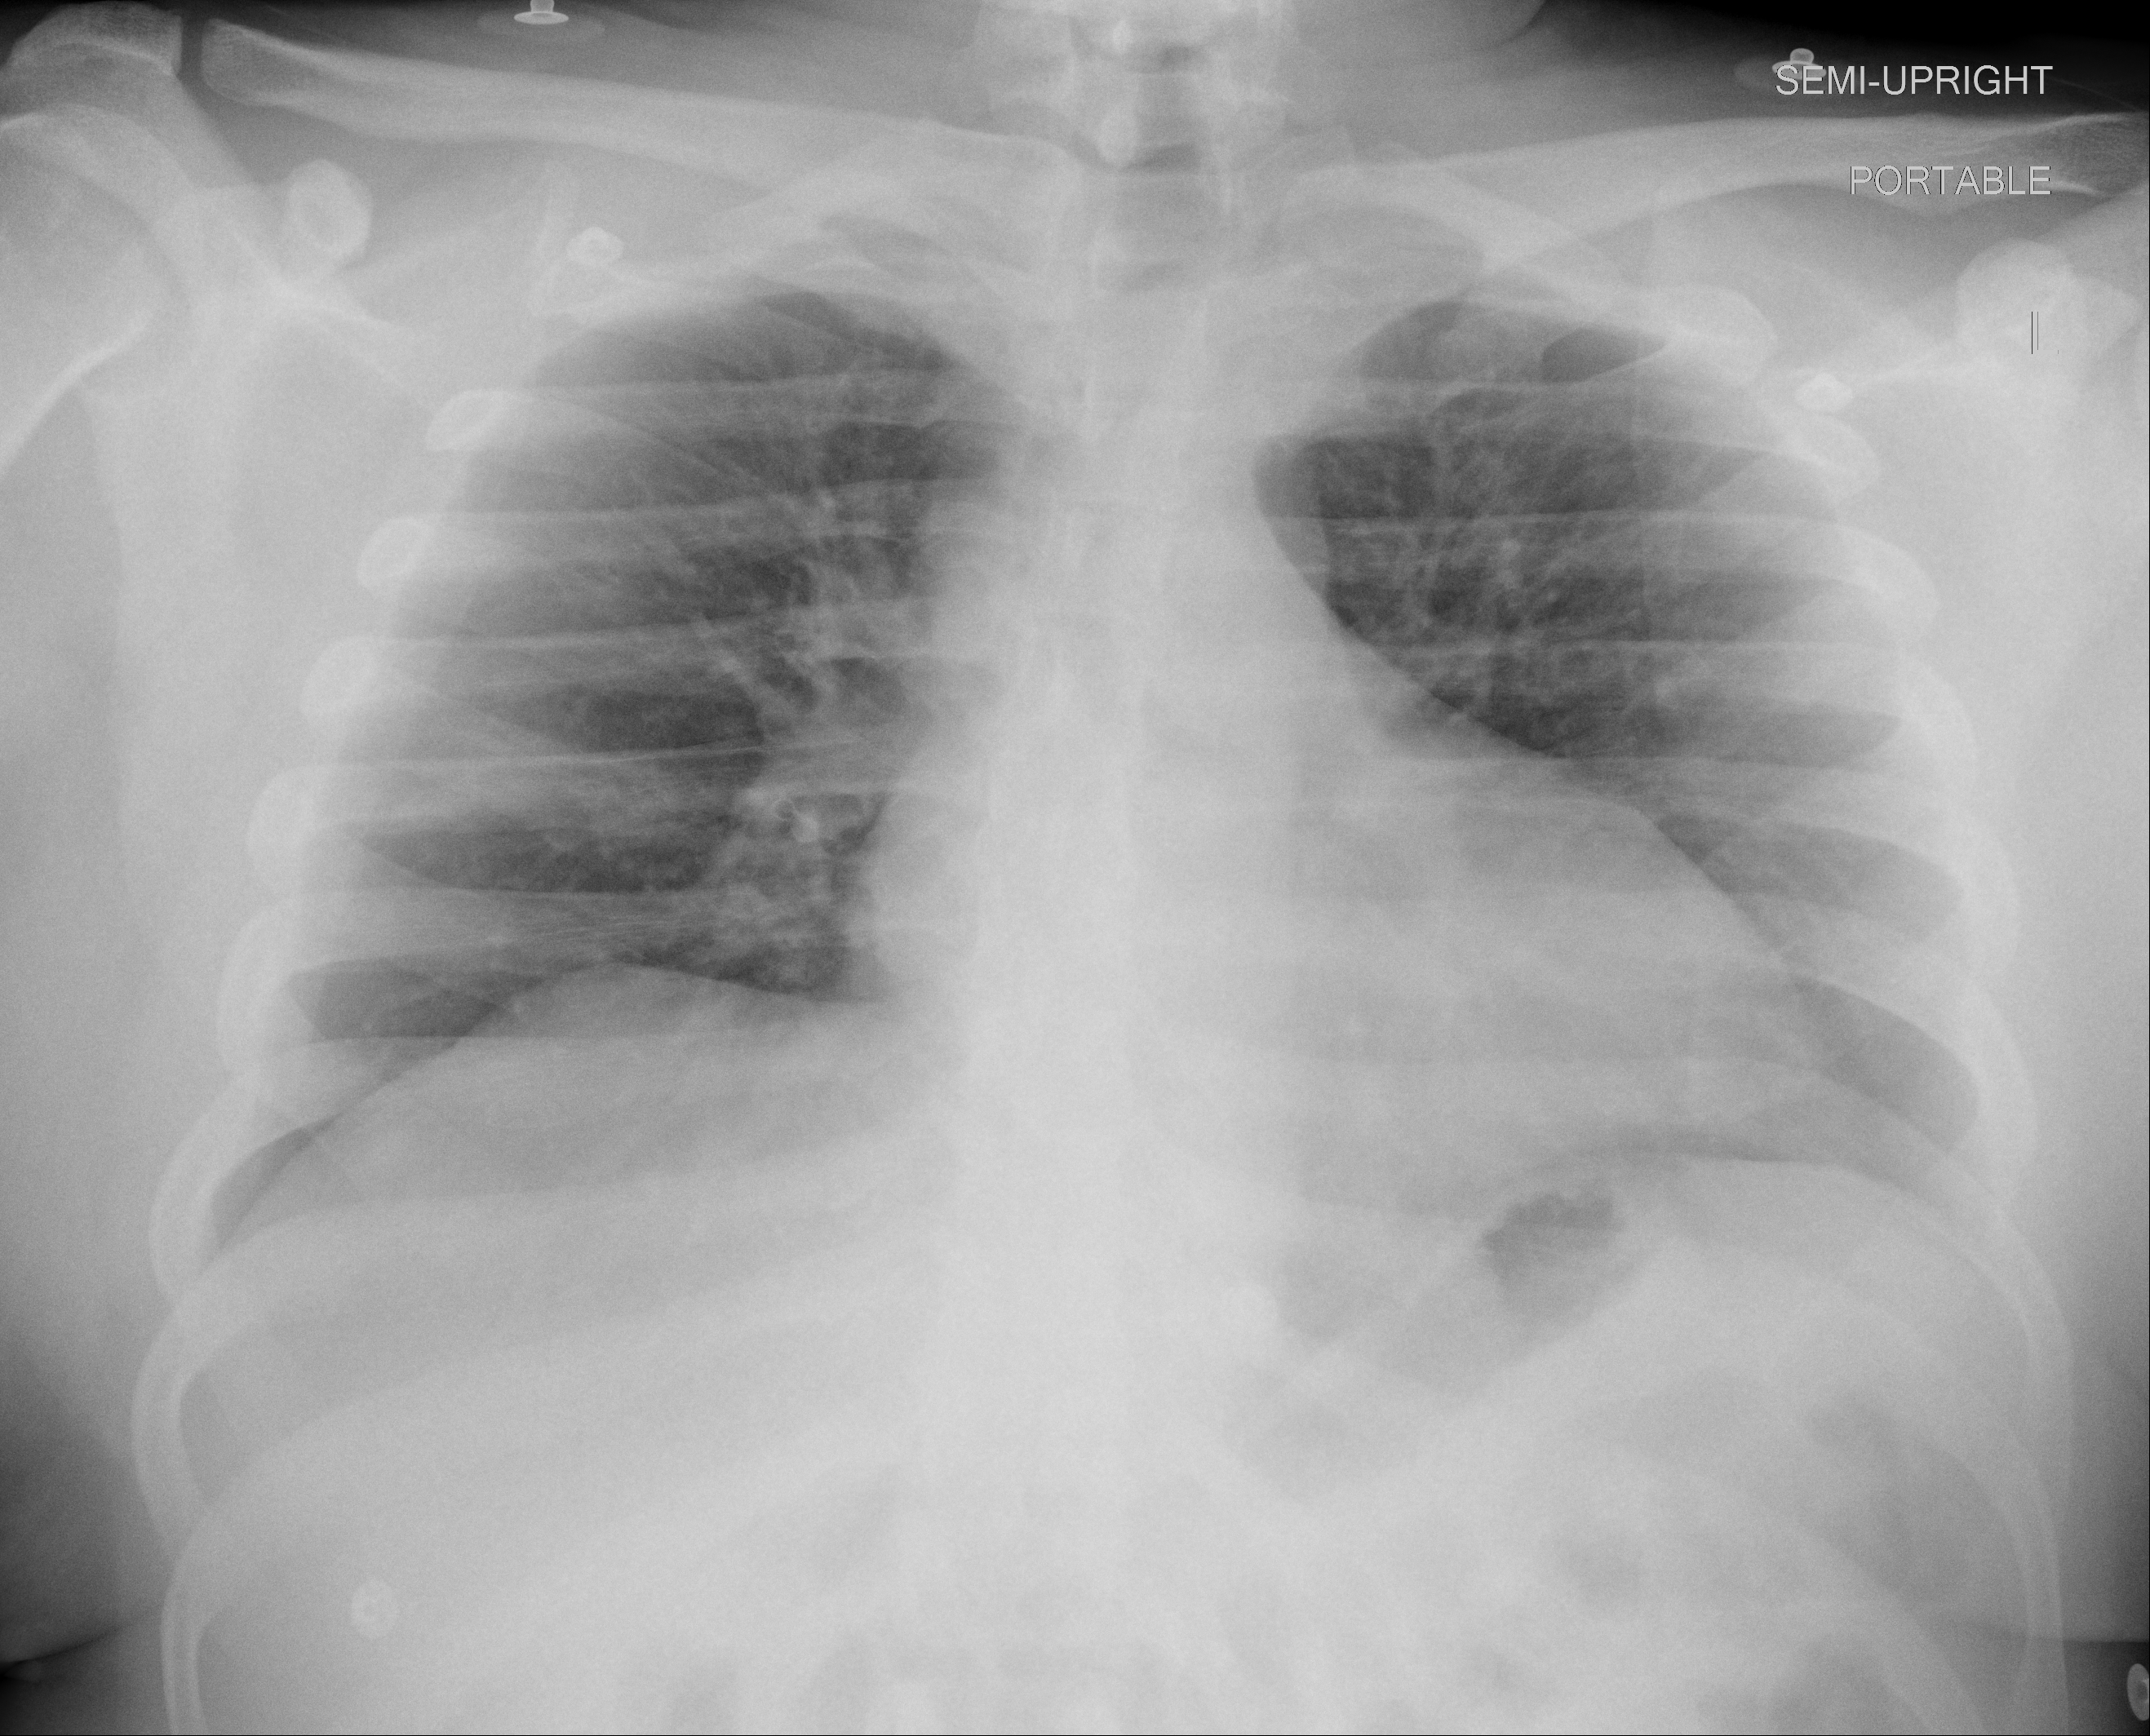
Chest X-ray (portable), AP projection. Male patient, age 43 years; imaged 0 days after the COVID-19 diagnosis.
Radiologist's key findings for this exam: The lungs are free of air space disease.